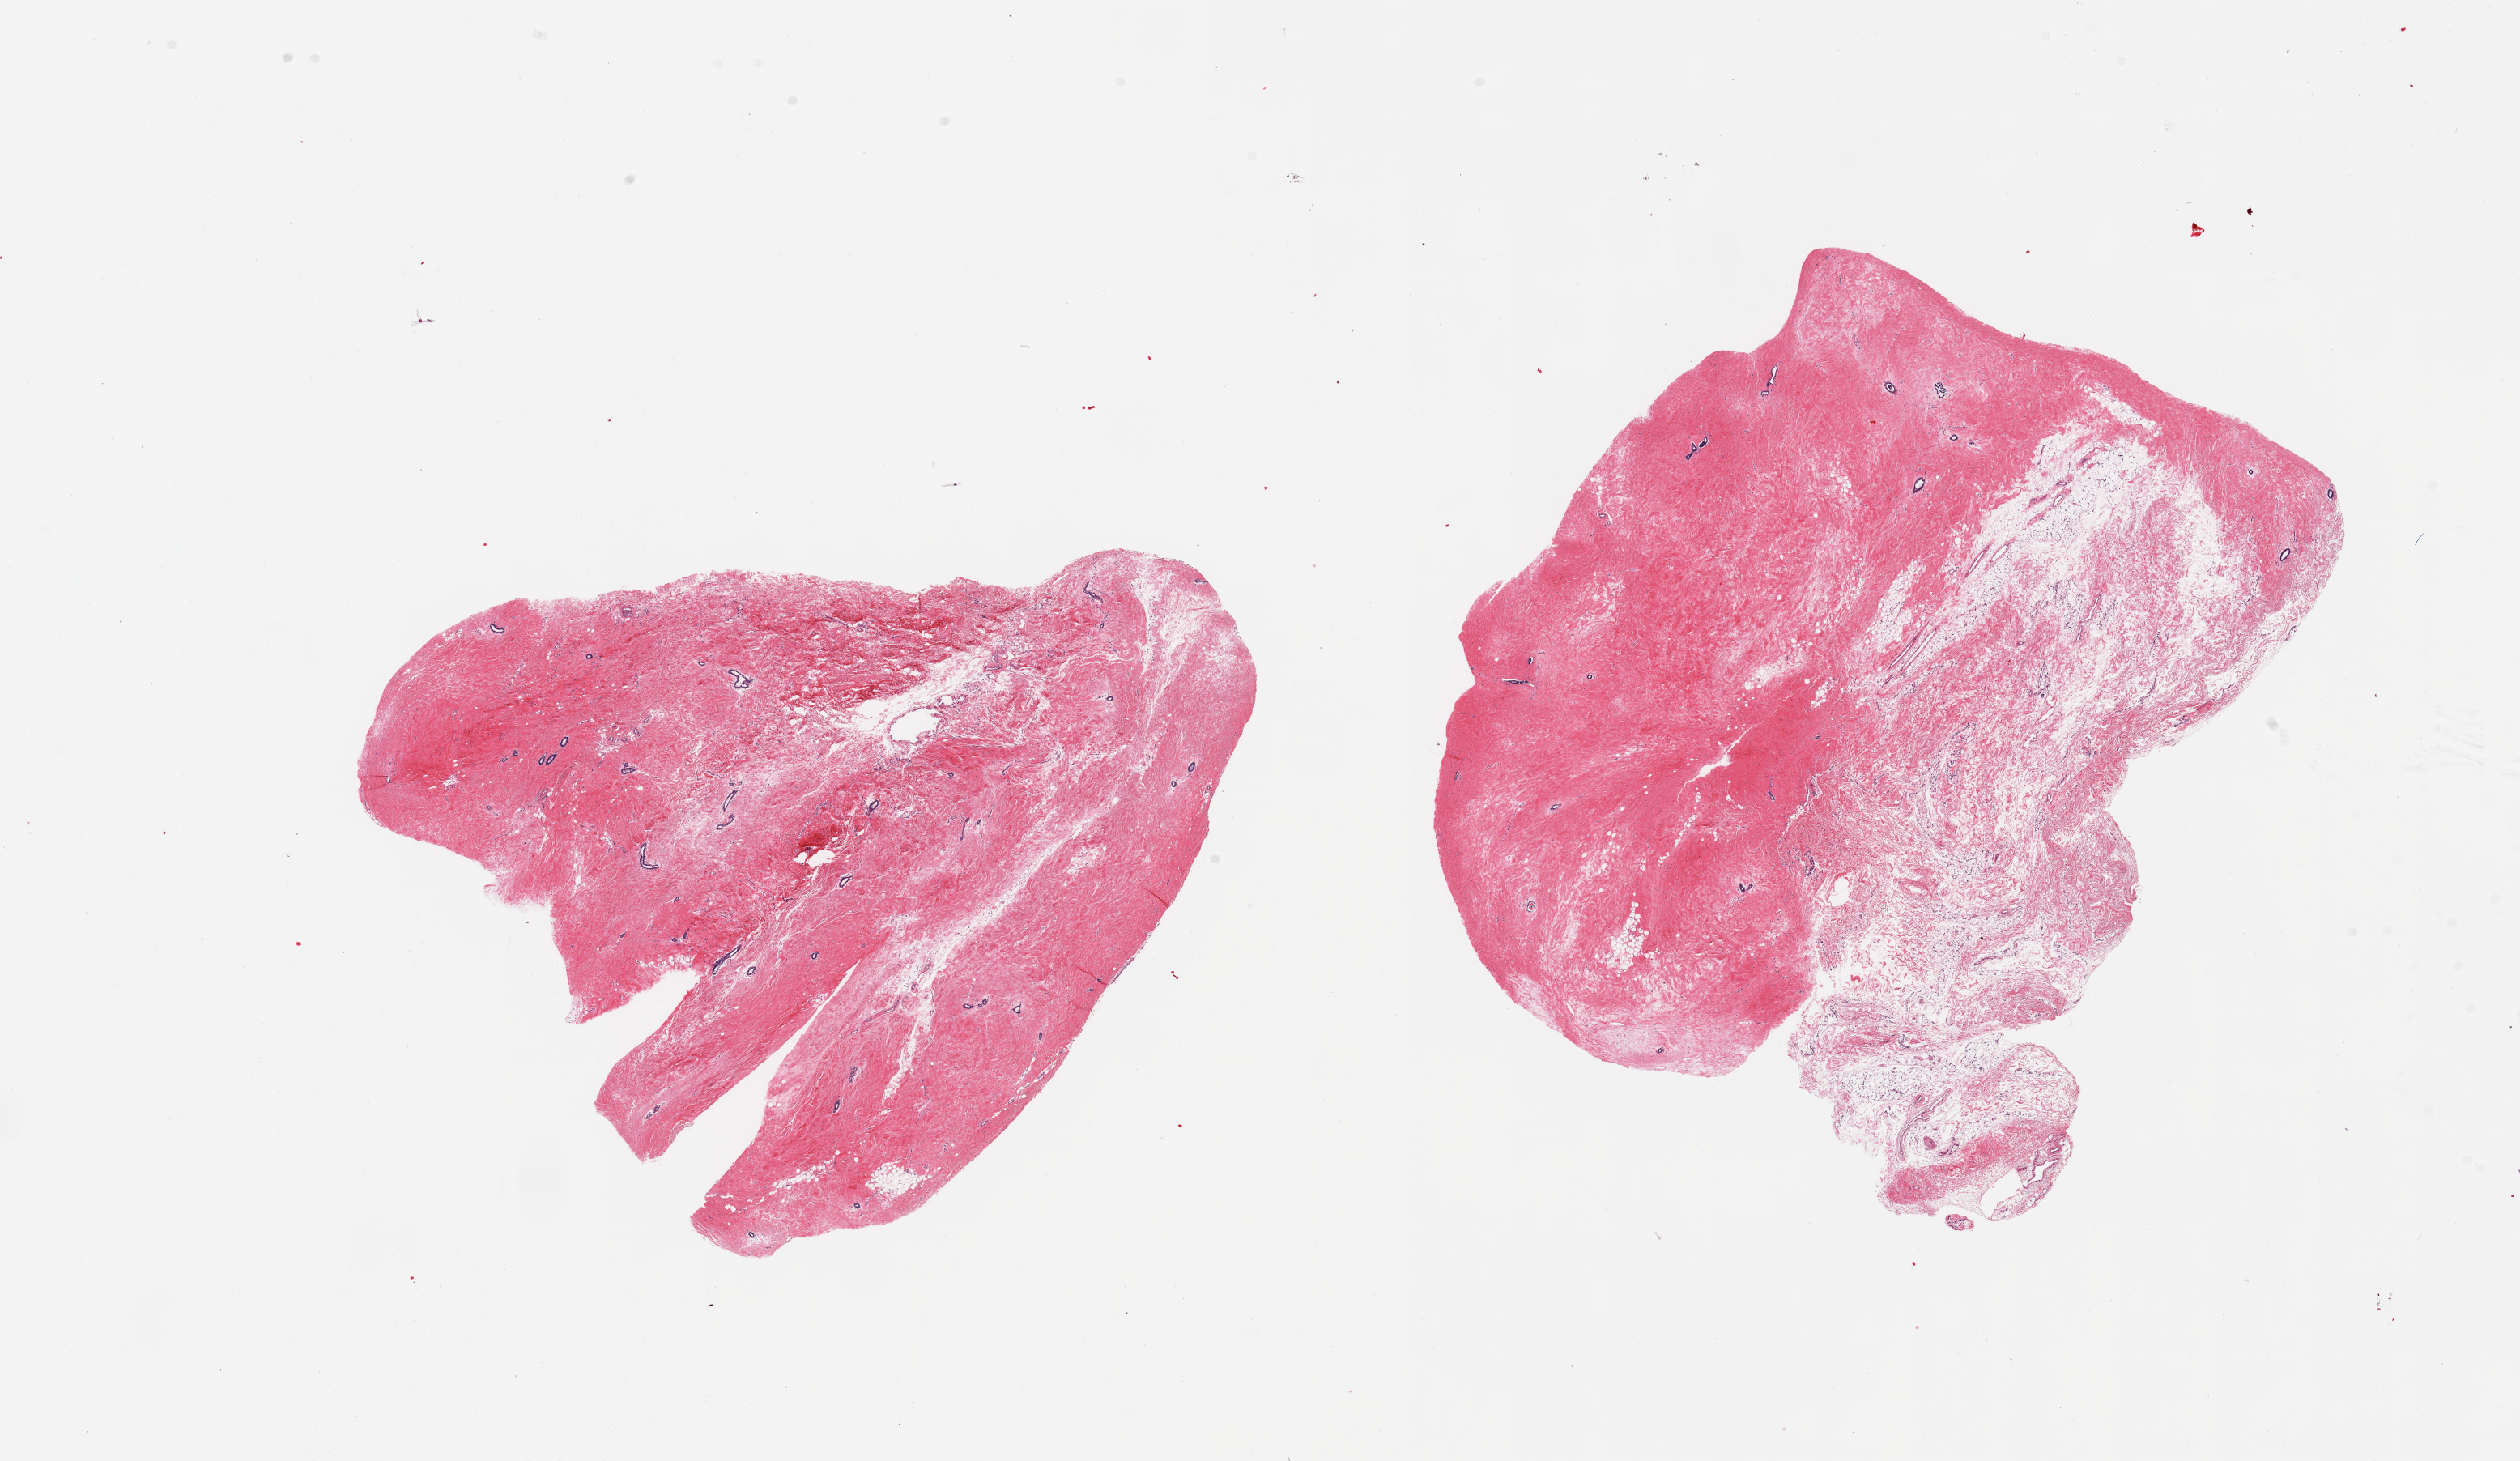
Digitized hematoxylin and eosin (H&E)-stained section — whole scanned area (about 24.6 x 14.3 mm) shown as a low-resolution overview, PAXgene-fixed paraffin-embedded (PFPE) section, sampled site (target tissue): breast, tissue donor sample. Donor sex: male.
- pathologist's review note for this sample: 2 pieces; gynecomastoid changes: 60% fibrous, 40% fat; atrophic ducts